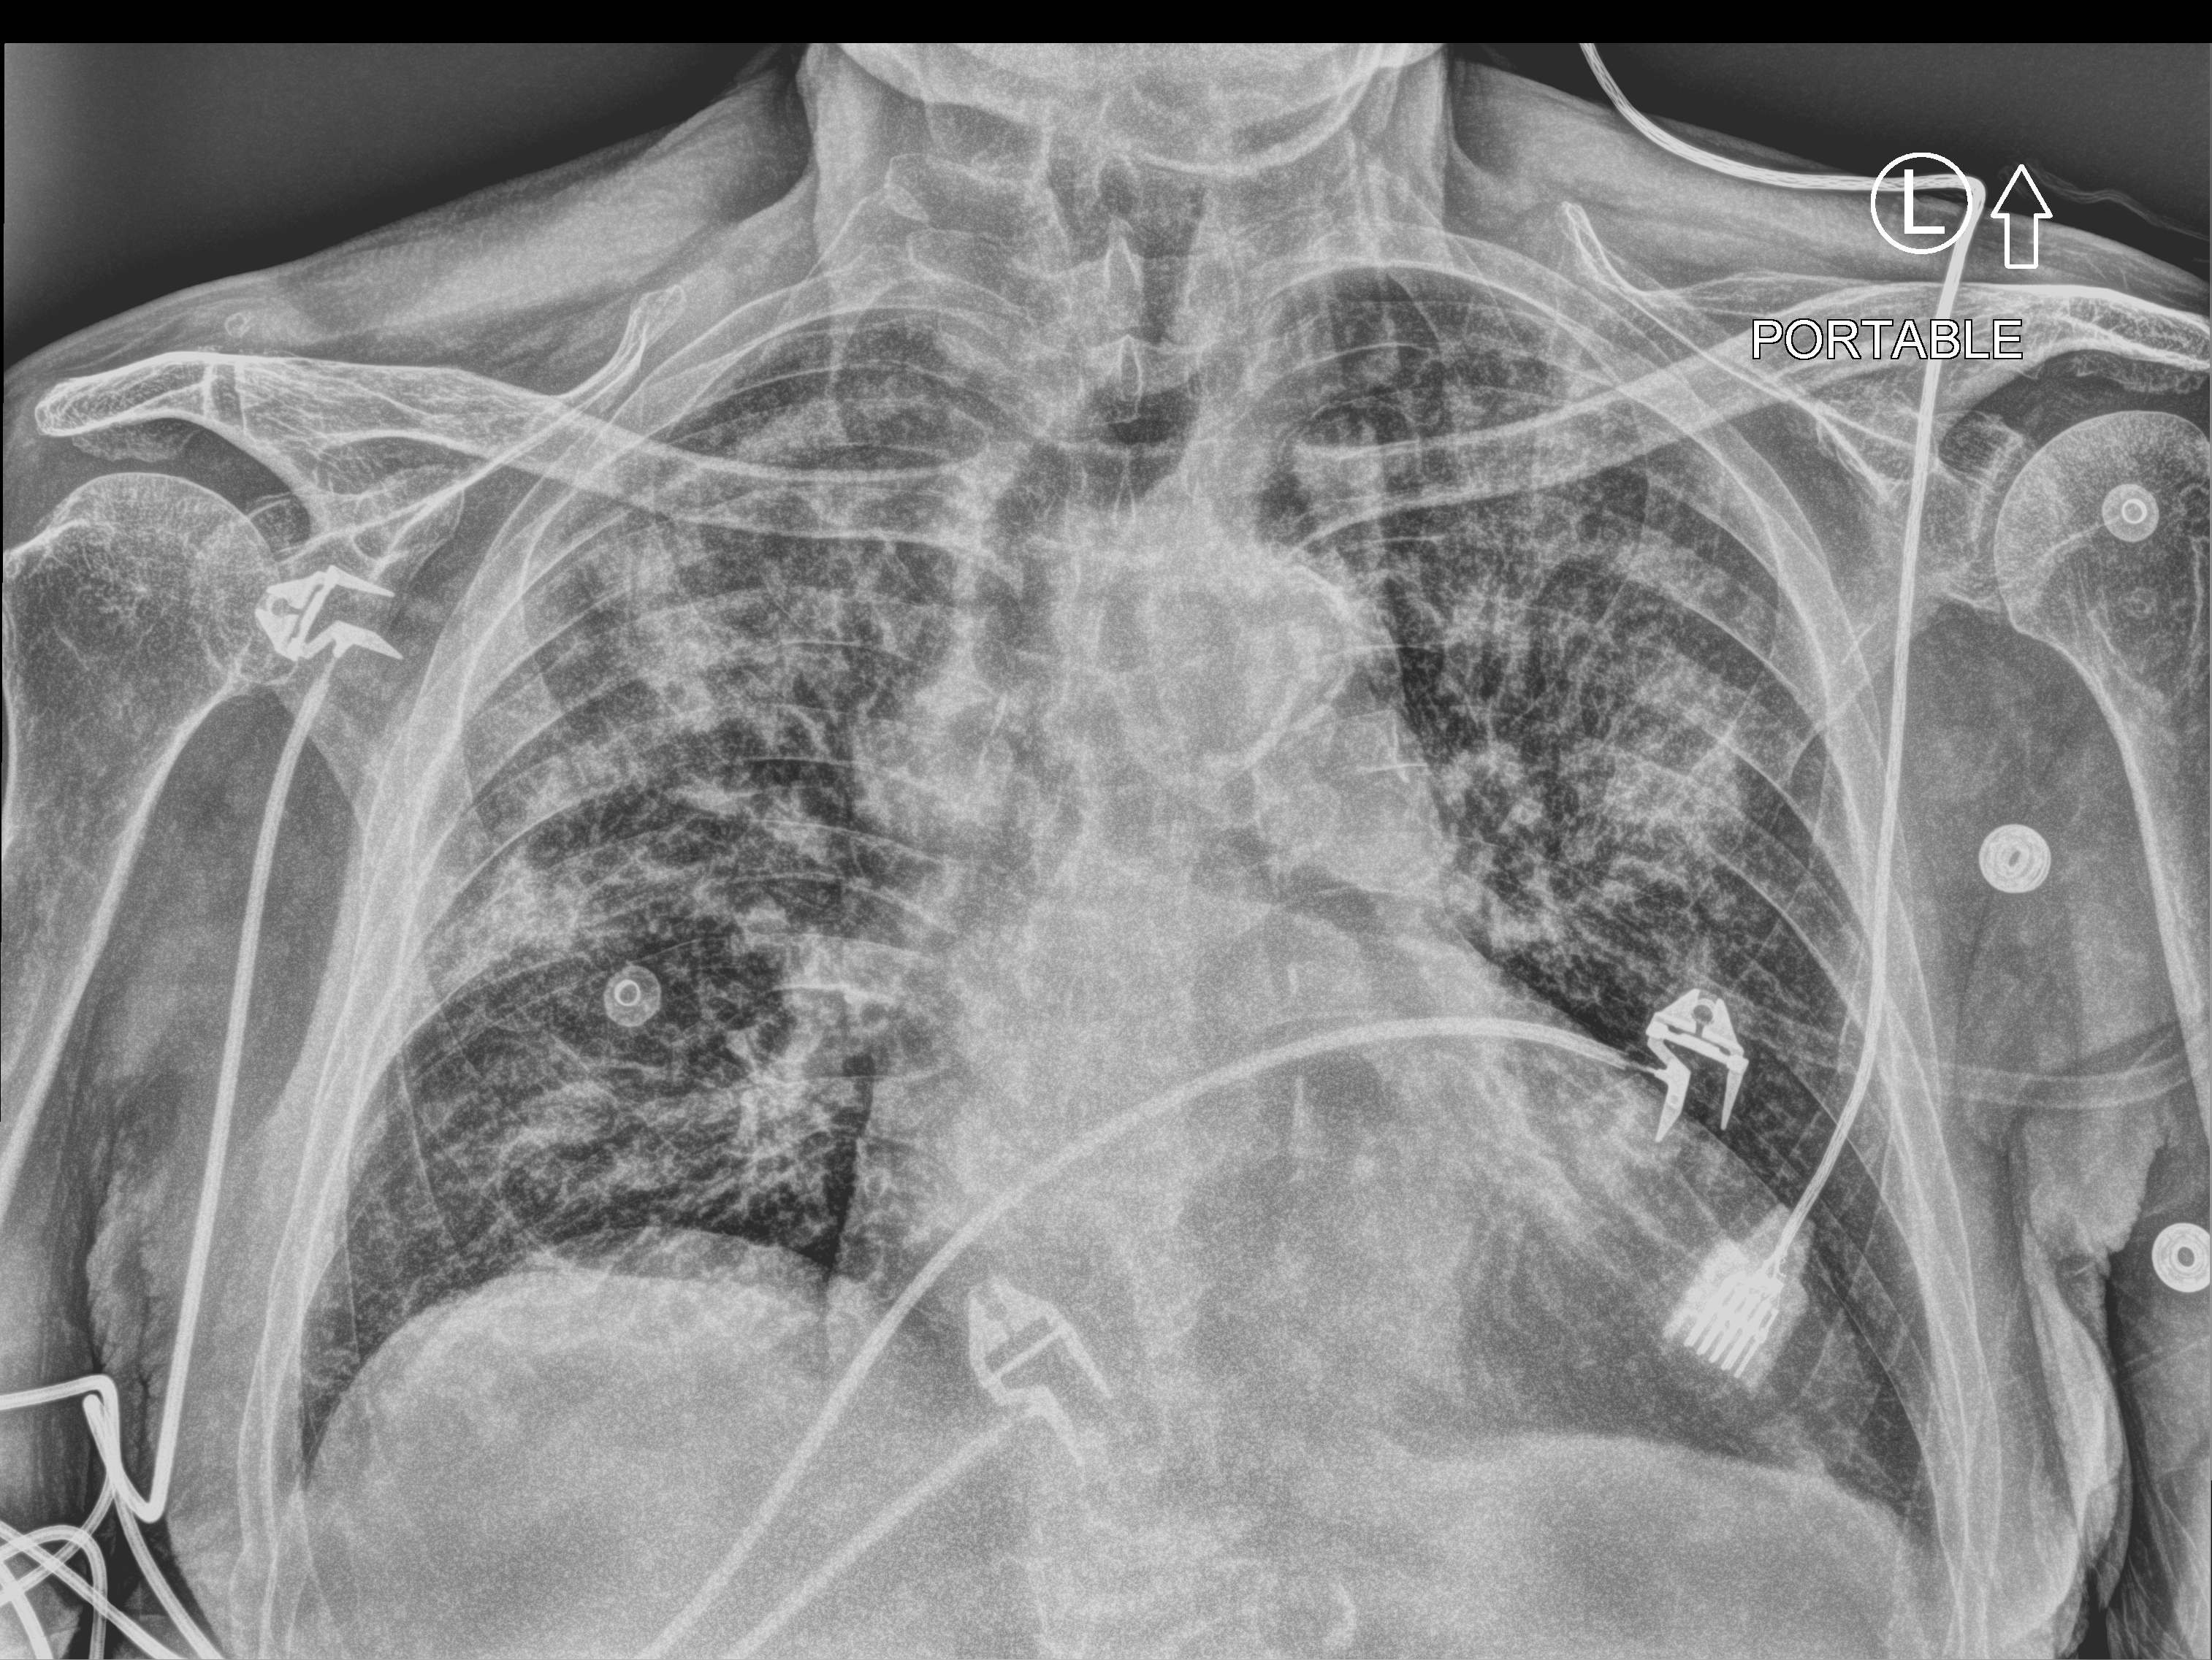
Portable chest radiograph. Male patient hospitalised with COVID-19, age 75–90 years.
From the hospital-stay record, not from the radiograph (when in the stay this image was taken is not recorded): admitted to intensive care during this hospital stay: no; mechanically ventilated during this hospital stay: no.